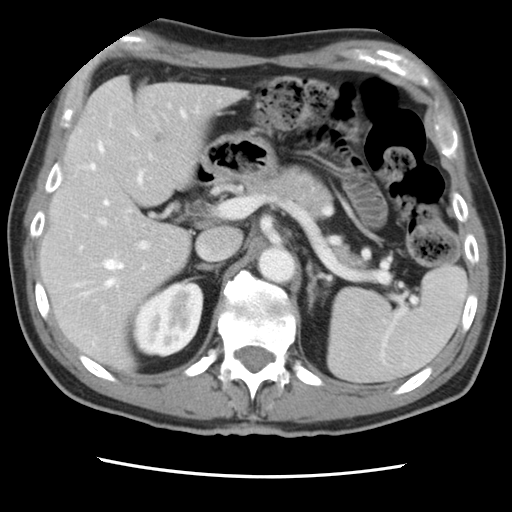
Contrast-enhanced abdominal CT, one axial slice. Position 51 of 83 along the scan axis. 120 kVp. Intravenous contrast given. Soft-tissue window (W 400 / L 40 HU). 5 mm slice thickness. 512 × 512 image matrix, field of view 321 × 321 mm. Male patient, age 69 years. Case-level facts recorded for this patient, not image findings: diagnosis: colorectal cancer liver metastases, imaged before liver resection; multiple liver metastases: yes; largest metastasis: 3.5 cm.
Annotated regions visible in this slice (expert manual segmentation):
- hepatic veins: bounding box [x1, y1, x2, y2] px = [92, 111, 186, 287]
- liver: [43, 78, 238, 368]
- planned liver remnant (the part of the liver to remain after resection): [43, 136, 190, 368]
- portal vein (with intrahepatic branches): [79, 155, 231, 309]